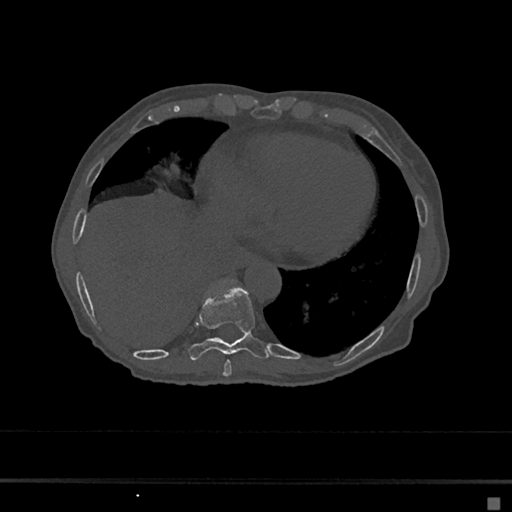
CT including the spine, one axial slice; position 273 of 797 along the scan axis; reconstruction kernel Br40s/3; bone window (W 1800 / L 400 HU); 0.5 mm slice thickness; 512 × 512 image matrix, field of view 360 × 360 mm. Patient: female, 68 years. From the clinical record (not read from this slice): primary cancer: renal.
Structures marked on this image (semi-automatic segmentation, software-assisted and operator-edited):
- T8 vertebra: bounding box (x1, y1, x2, y2) in pixels: (223, 360, 232, 377)
- T9 vertebra: (187, 286, 271, 361)